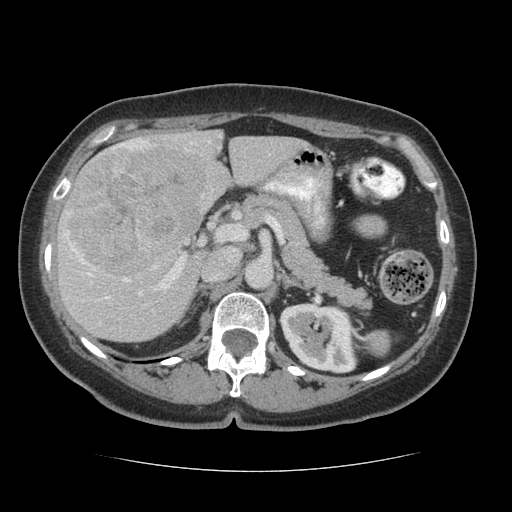
Contrast-enhanced abdominal CT (liver protocol), one axial slice; slice 34 of 75 in the series (ordered by position); reconstruction kernel STANDARD; soft-tissue window (W 400 / L 40 HU); 2.5 mm slice thickness; 512 × 512 image matrix, field of view 360 × 360 mm. From the clinical record (not read from this slice): diagnosis: hepatocellular carcinoma (patient treated with transarterial chemoembolisation; whether this scan precedes or follows treatment is not stated here); TNM stage (as recorded): Stage-I; Child-Pugh class: A; tumour nodularity: uninodular.
Annotated regions visible in this slice (semi-automatic segmentation, software-assisted and operator-edited):
- liver parenchyma outside the tumour (the mass and vessels are separate outlines, so this box may not span the whole liver): box from (x=56, y=130) to (x=307, y=340) px
- mass: (x=64, y=146)–(x=204, y=280)
- liver vessels: (x=63, y=135)–(x=221, y=301)